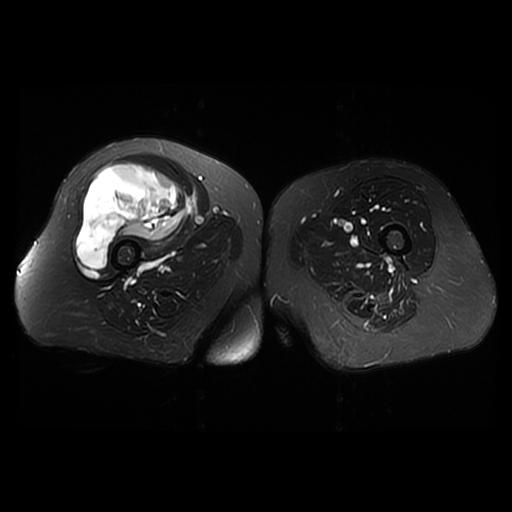
MRI of an extremity soft-tissue mass, one axial slice; slice 25 of 42 in the series (ordered by position); T2-weighted fat-saturated; 6 mm slice thickness; 512 × 512 image matrix. Female patient. Case-level facts recorded for this patient, not image findings: histological type: pleiomorphic undifferentiated sarcoma; grade: high; site of the primary tumour: right quadricep.
Annotated regions visible in this slice (outlined manually by an expert reader):
- gross tumour volume including surrounding oedema: bounding box (x1, y1, x2, y2) in pixels: (76, 164, 187, 269)
- gross tumour volume (mass): (76, 164, 187, 269)